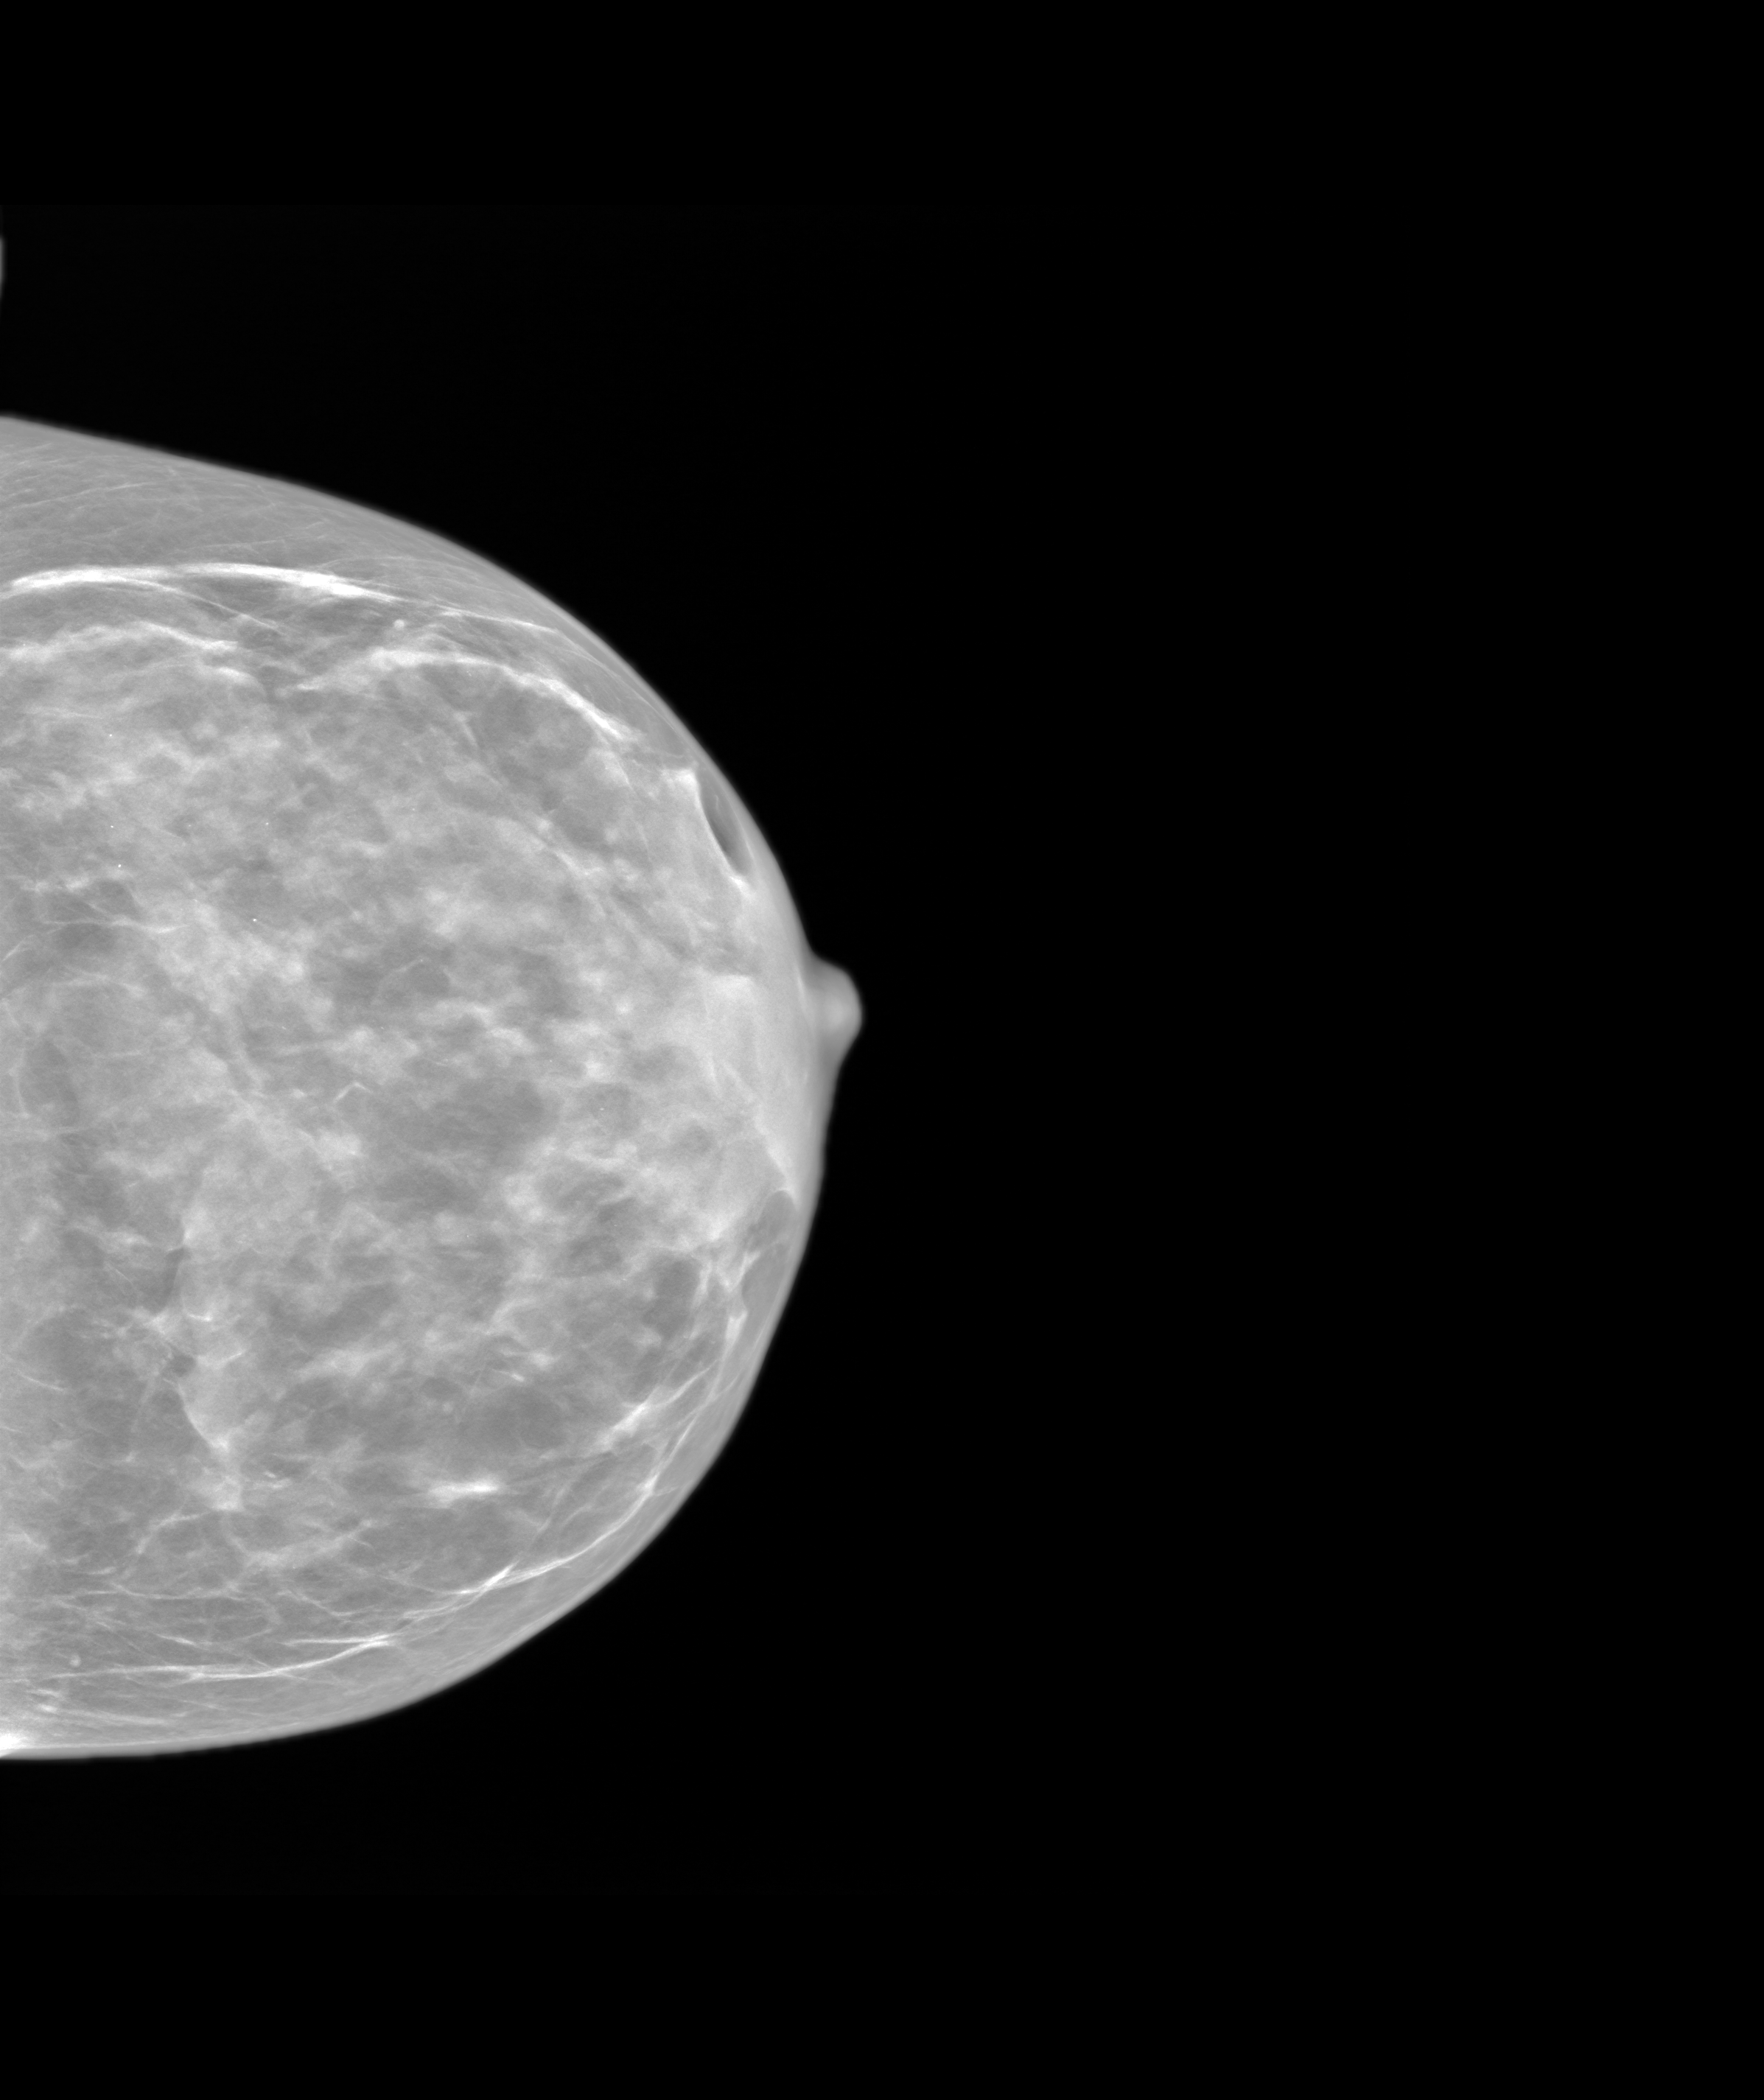
Synthesized 2-D mammogram reconstructed from digital breast tomosynthesis; left breast; cranio-caudal projection; annual screening mammography examination; system: SenoIris_1SP1.1(421). Patient: female, 47 years.
- BI-RADS breast density category at the screening exam (both breasts, scale 1–4): 3
- final BI-RADS assessment for this screening round (tomosynthesis exam, both breasts): category 3
- recall: recalled for additional imaging after this screen